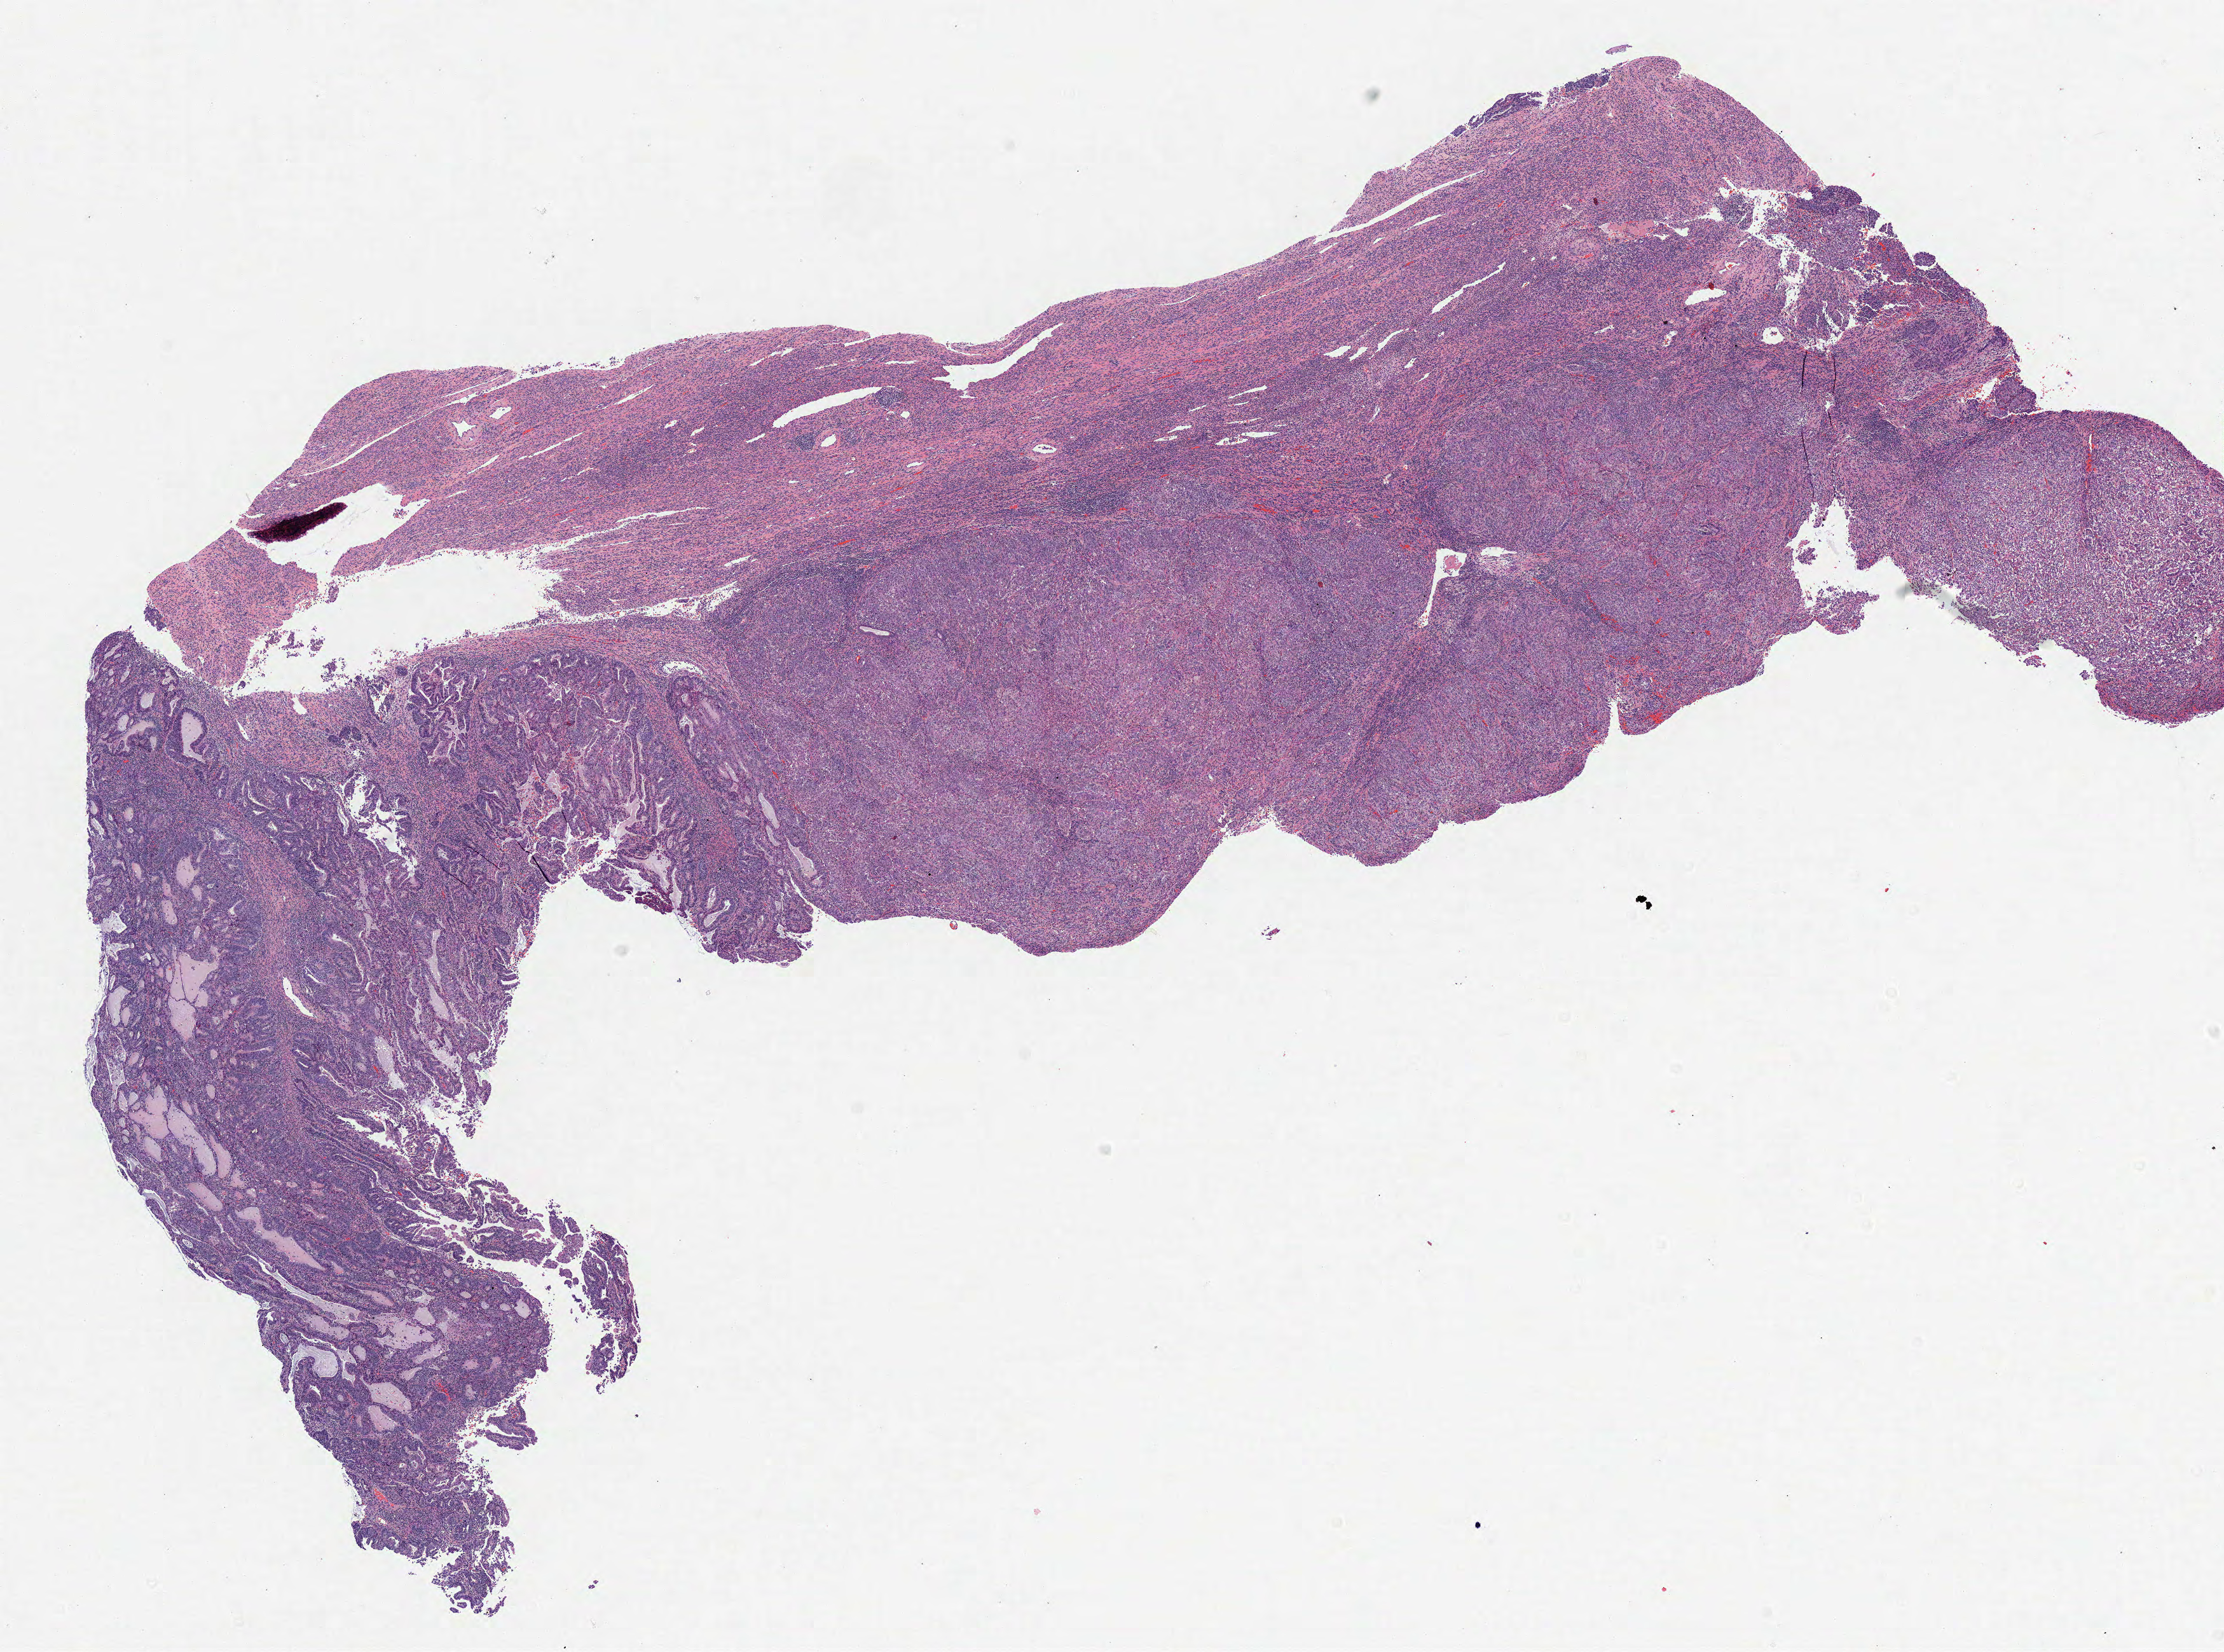
H&E whole-slide image — shown as a low-resolution overview of the whole scanned area (about 14.0 x 10.4 mm); formalin-fixed paraffin-embedded (FFPE) diagnostic section; uterus, primary tumour sample. Patient sex: female. Histologic grade: G3 (poorly differentiated).
• FIGO stage: IC
• pathologic diagnosis: Endometrioid adenocarcinoma, NOS (endometrium)